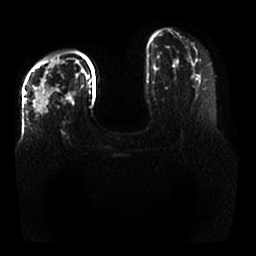
Breast MRI, one axial slice. Slice 14 of 25 in the series (ordered by position). Diffusion-weighted series; image 2 of 4 stored at this slice position (different b-values; order by instance number). 1.5 T. 4 mm slice thickness. 256 × 256 image matrix, field of view 350 × 350 mm. Female patient.
Structures marked on this image (expert manual segmentation):
- tumour on diffusion-weighted imaging: bounding box [x1, y1, x2, y2] px = [33, 59, 59, 114]